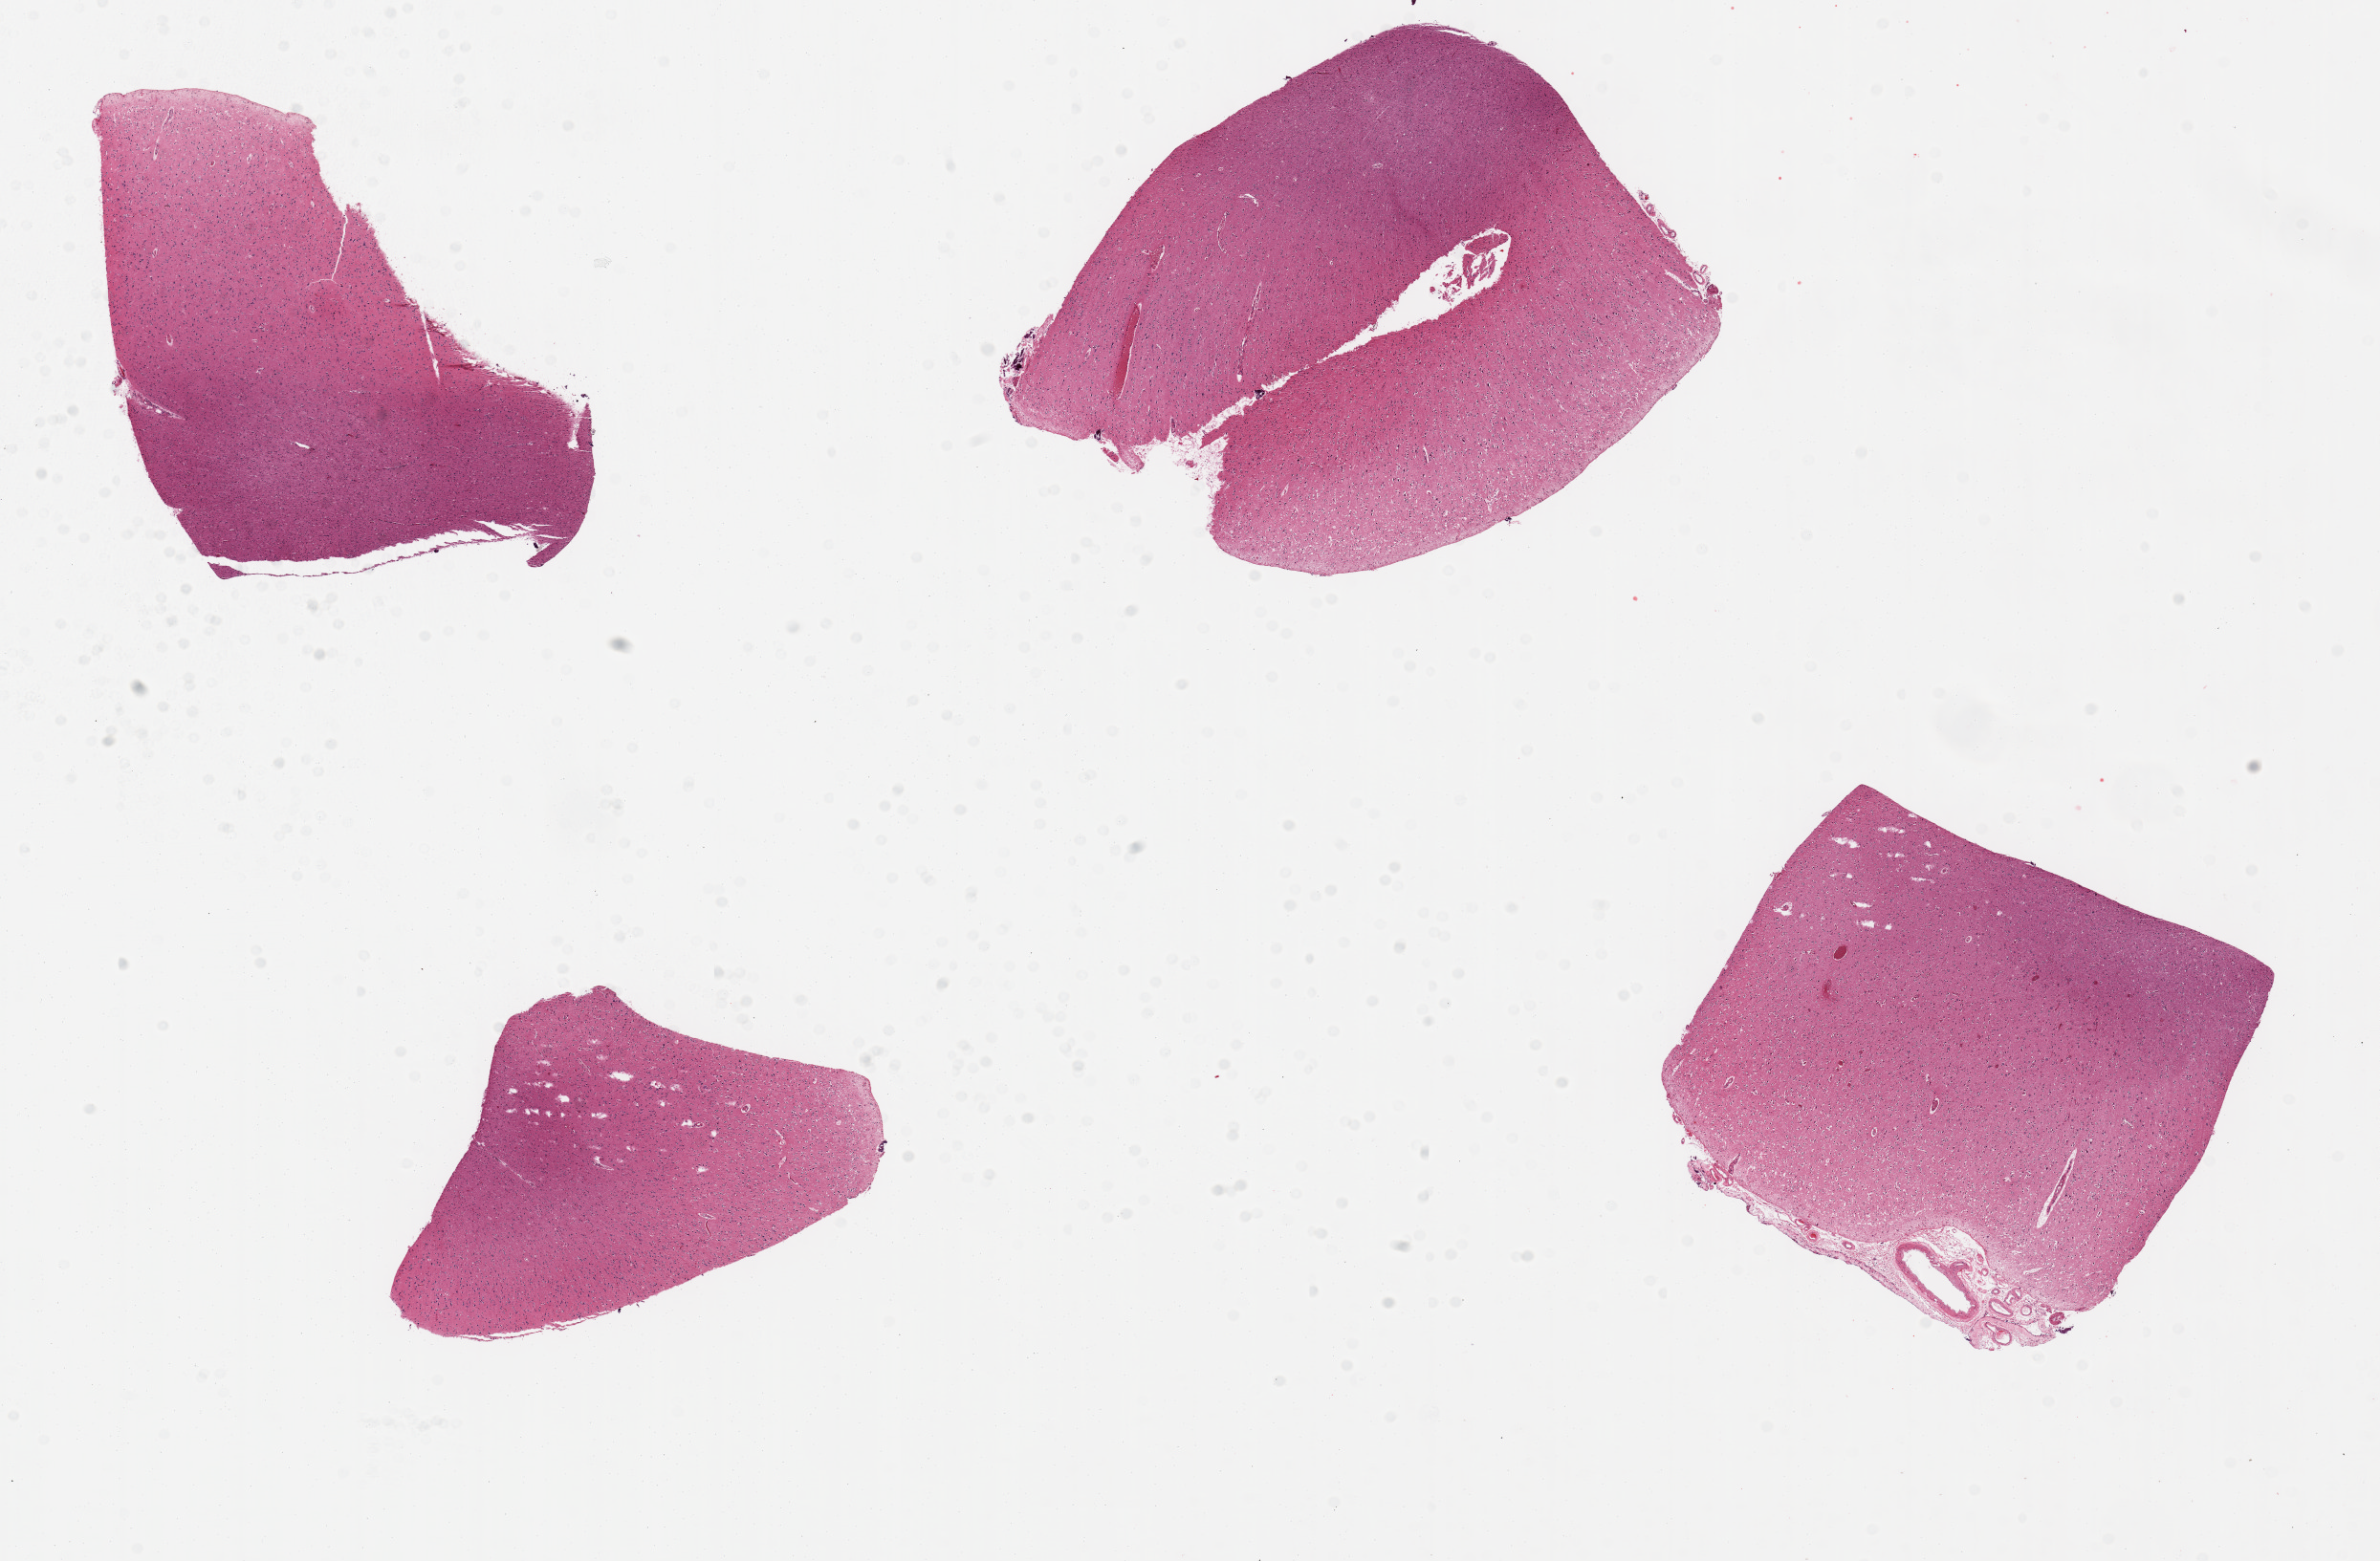
Whole-slide image, hematoxylin and eosin (H&E) stain, brightfield, whole scanned area (about 19.7 x 12.9 mm, slide scanned at 20x) shown as a low-resolution overview; PAXgene-fixed, paraffin-embedded tissue; target tissue: cerebral cortex; donor tissue sample. Donor: female.
Review note (as recorded): 4 ~4x4mm aliquots.